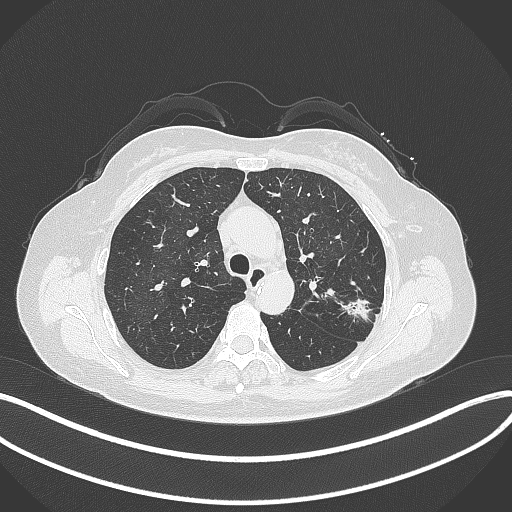
Chest CT, one axial slice. Reconstruction kernel B70f. 120 kVp. Lung window (W 1500 / L -600 HU). 1 mm slice thickness. 512 × 512 image matrix, field of view 400 × 400 mm. Patient: female, 60 years. From the clinical record (not read from this slice): clinical TNM (as recorded): T1c N0 M0.
Outlined on this slice (rectangle marked by the reading radiologist):
- lung tumour (recorded histology: adenocarcinoma): bounding box [x1, y1, x2, y2] px = [340, 294, 377, 326]